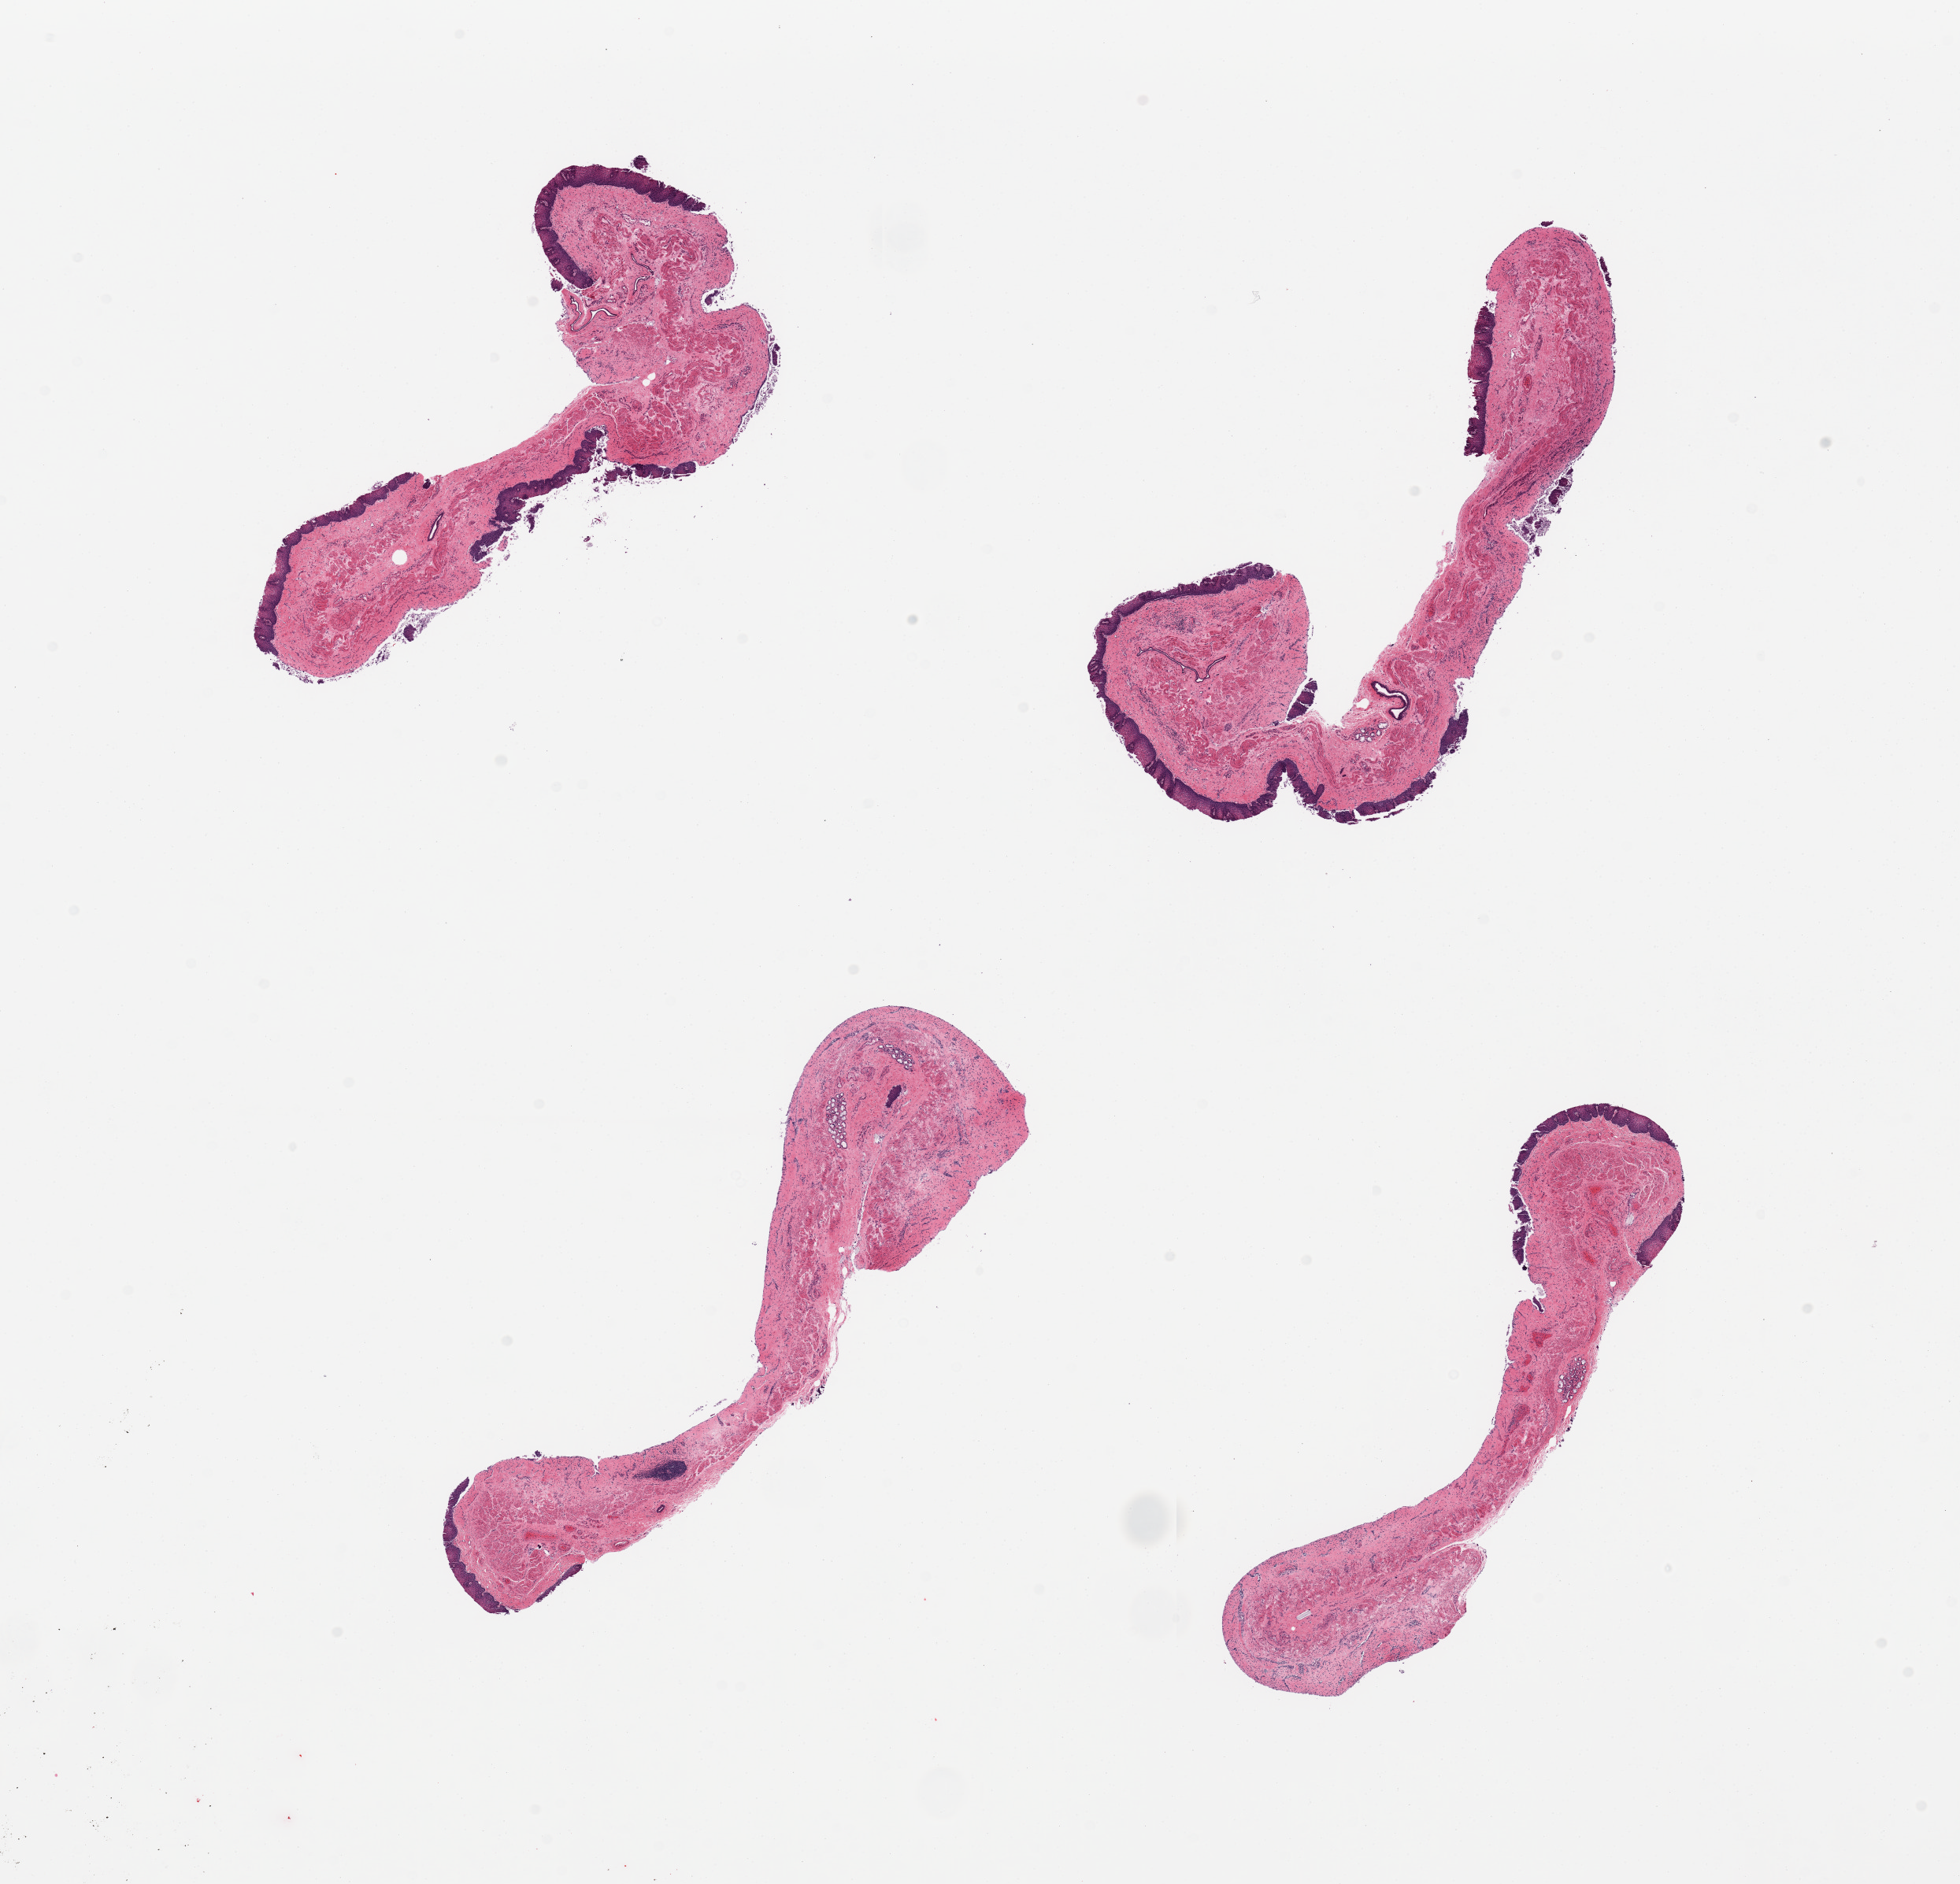
Digitized hematoxylin and eosin (H&E)-stained section, whole scanned area (about 19.7 x 18.9 mm) shown as a low-resolution overview; PAXgene-fixed paraffin-embedded (PFPE) section; section of esophageal mucous membrane (target tissue); tissue donor sample. Donor sex: female.
• reviewer comment on this tissue sample: 4 pieces; partial sloughing of epithelium; glandular atrophy and squamous metaplasia of glandular ducts